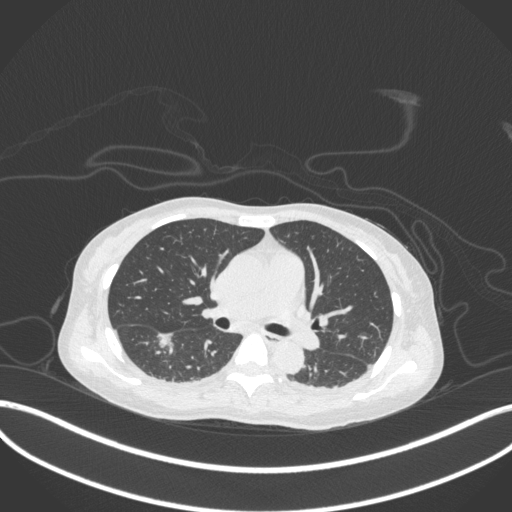
Chest CT, one axial slice; slice 181 of 260 in the series (ordered by position); reconstruction kernel B31f; 120 kVp; lung window (W 1500 / L -600 HU); 1 mm slice thickness; 512 × 512 image matrix, field of view 400 × 400 mm. Female patient, age 44 years. Case-level facts recorded for this patient, not image findings: clinical TNM (as recorded): T1c N0 M0.
Annotated regions visible in this slice (bounding box drawn by a radiologist):
- lung tumour (recorded histology: adenocarcinoma): bounding box <153,326,177,350> (left, top, right, bottom; pixels)